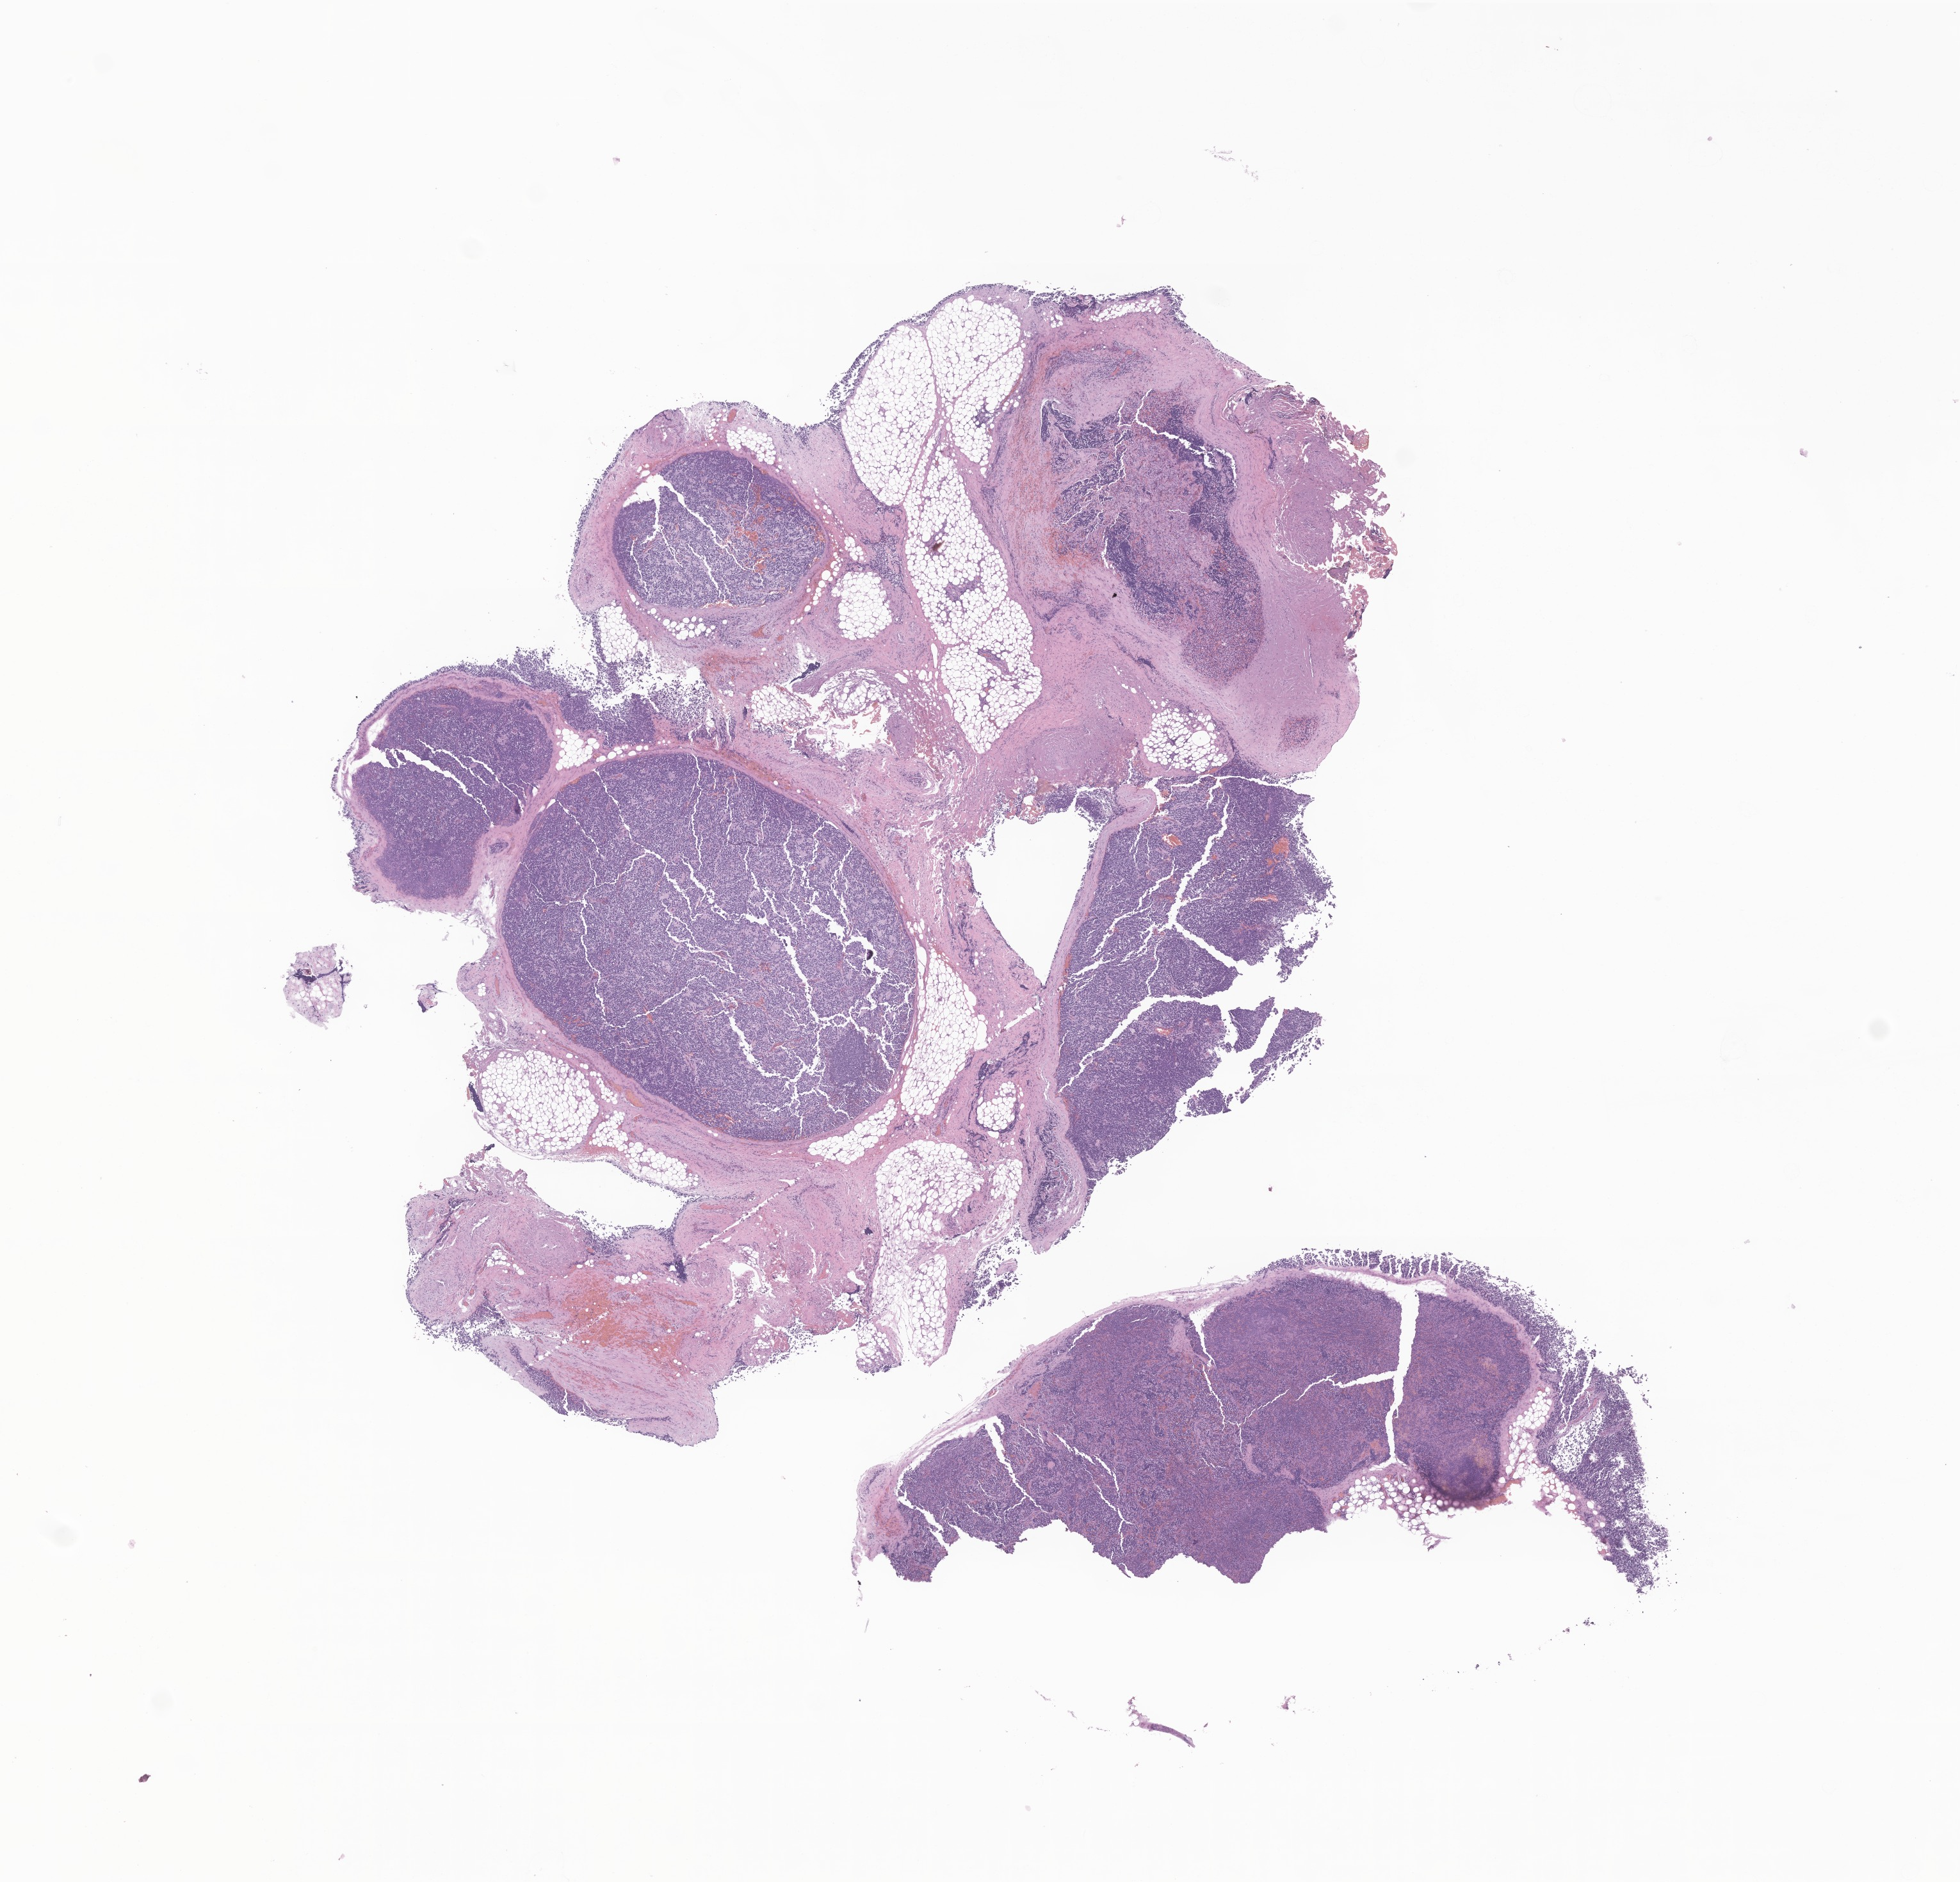
Digitized H&E-stained section of tumor tissue from the retroperitoneum, a low-resolution overview of the entire scanned area, about 12.9 x 12.4 mm. FFPE section. Patient male; age 70 months.
Diagnosis (ICD-O-3 morphology term): Neuroblastoma, NOS.